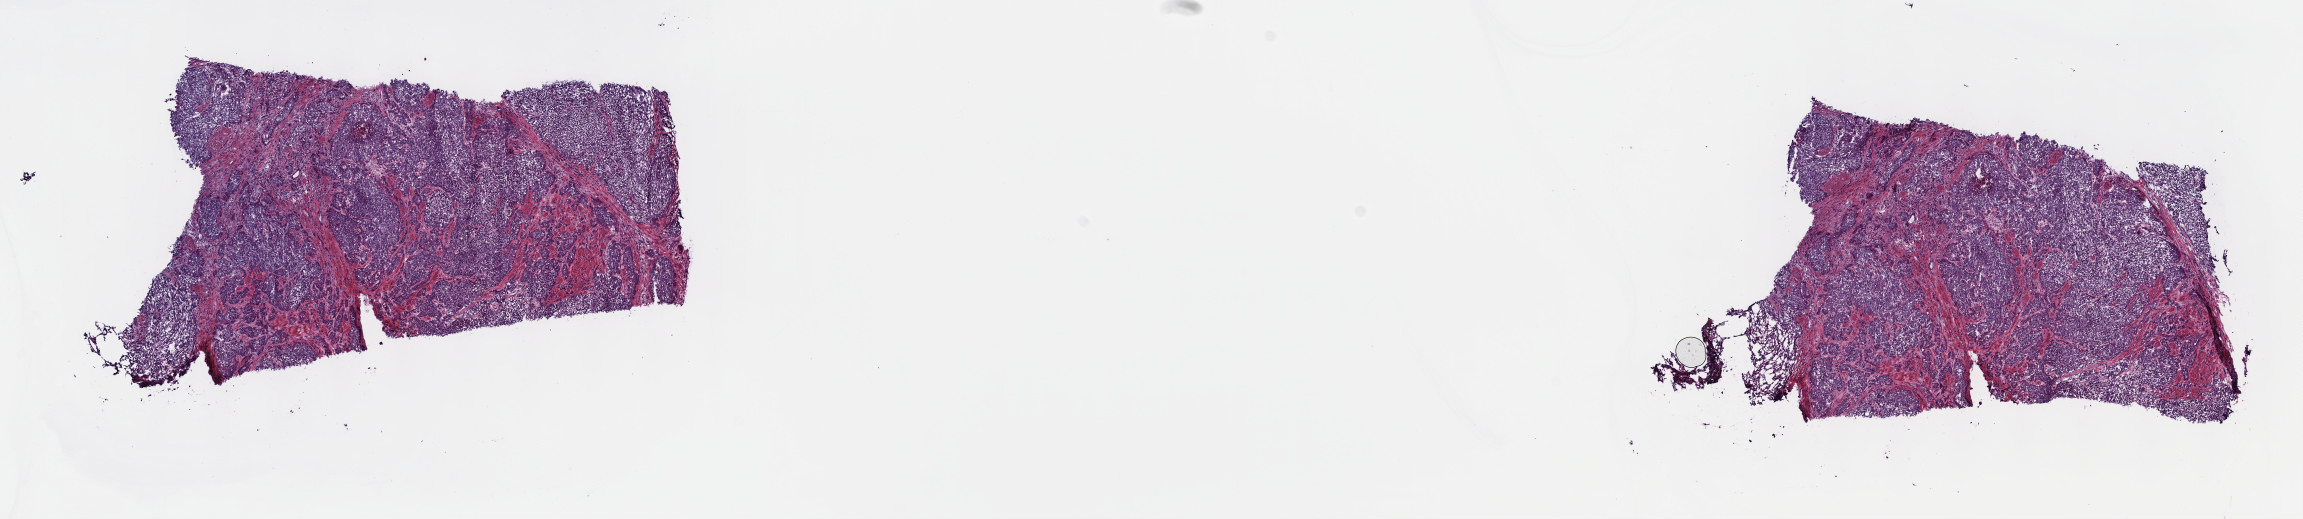
Digitized H&E-stained tissue section (whole slide), whole scanned area (about 18.6 x 4.2 mm) shown as a low-resolution overview. Frozen section. Primary tumour sample from the bladder. Patient: male, age at initial diagnosis 85 years. Histologic grade: high grade. Composition of this section per pathologist review: tumour cells 70%, tumour nuclei 70%, normal cells 0%, stromal cells 30%, necrosis 0%. Infiltration values recorded for this section: lymphocyte infiltration 5%, monocyte infiltration 0%, neutrophil infiltration 0%.
Diagnosis: Papillary transitional cell carcinoma. AJCC pathologic stage: III (6th edition). TNM: T3b N0 M0.